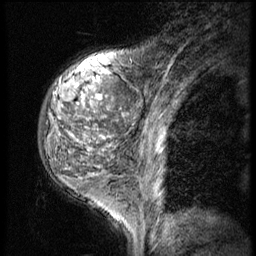
Breast MRI (dynamic contrast-enhanced), one sagittal slice; position 14 of 56 along the scan axis; 3 images stored at this slice position (order not interpretable as contrast timing); 1.5 T; TE 4.2 ms, TR 9 ms; 256 × 256 image matrix. Female patient, age 50 years. From the clinical record (not read from this slice): setting: breast cancer imaged before/during neoadjuvant chemotherapy; receptor status: triple-negative.
Annotated regions visible in this slice (semi-automatically segmented with operator editing):
- analysis volume of interest (the breast-tissue region the enhancement analysis was run in; not a lesion): bounding box [x1, y1, x2, y2] px = [37, 50, 116, 191]
- tumour enhancement mask (voxels above the 140 % enhancement threshold inside the analysis volume of interest): [53, 93, 102, 99]